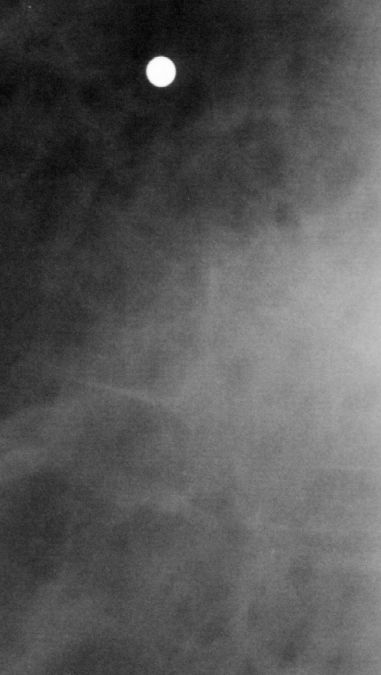
Cropped region of a digitized screen-film mammogram centred on a radiologist-marked abnormality, right breast, MLO view.
Marked abnormality: mass, shape oval, margins ill defined; BI-RADS assessment category 5; pathology result (as recorded, not read from the image): malignant.